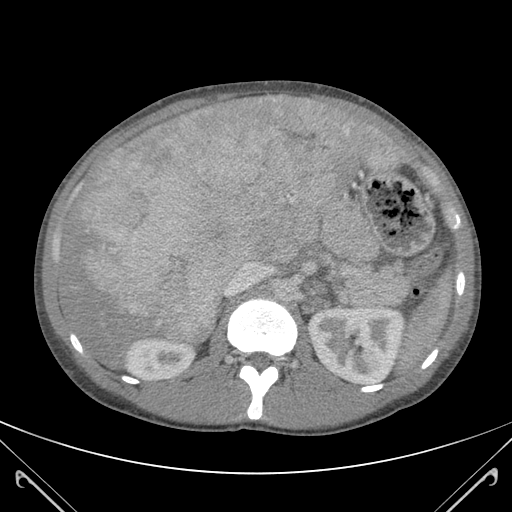
Contrast-enhanced abdominal CT (liver protocol), one axial slice; position 70 of 118 along the scan axis; 120 kVp; soft-tissue window (W 400 / L 40 HU); 512 × 512 image matrix, field of view 380 × 380 mm. Case-level facts recorded for this patient, not image findings: diagnosis: hepatocellular carcinoma (patient treated with transarterial chemoembolisation; whether this scan precedes or follows treatment is not stated here); TNM stage (as recorded): Stage-IIIB; Child-Pugh class: A; tumour nodularity: uninodular.
Structures marked on this image (semi-automatic segmentation, software-assisted and operator-edited):
- abdominal aorta: bounding box (x1, y1, x2, y2) in pixels: (276, 278, 298, 302)
- liver parenchyma outside the tumour (the mass and vessels are separate outlines, so this box may not span the whole liver): (58, 96, 390, 364)
- mass: (66, 97, 374, 341)
- liver vessels: (223, 98, 382, 296)